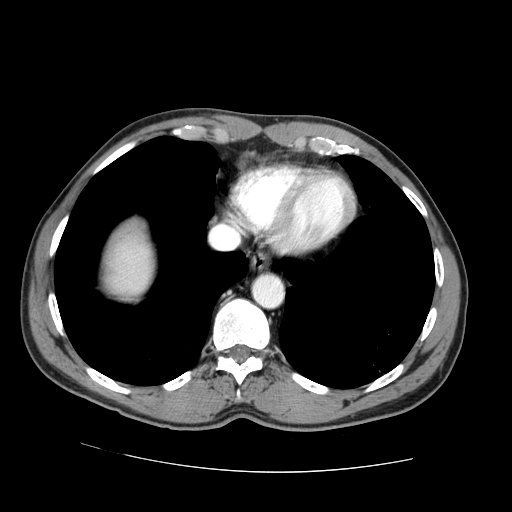
Contrast-enhanced abdominal CT (liver protocol), one axial slice; position 66 of 73 along the scan axis; reconstruction kernel STANDARD; 100 kVp; one of 2 acquisitions stored at this slice position; soft-tissue window (W 400 / L 40 HU); 2.5 mm slice thickness; 512 × 512 image matrix, field of view 380 × 380 mm. Case-level facts recorded for this patient, not image findings: diagnosis: hepatocellular carcinoma (patient treated with transarterial chemoembolisation; whether this scan precedes or follows treatment is not stated here); TNM stage (as recorded): Stage-IVA; Child-Pugh class: A; tumour differentiation: no biopsy; tumour nodularity: uninodular.
Structures marked on this image (semi-automatically segmented with operator editing):
- abdominal aorta: bounding box [x1, y1, x2, y2] px = [253, 275, 282, 307]
- liver parenchyma outside the tumour (the mass and vessels are separate outlines, so this box may not span the whole liver): [108, 230, 152, 294]